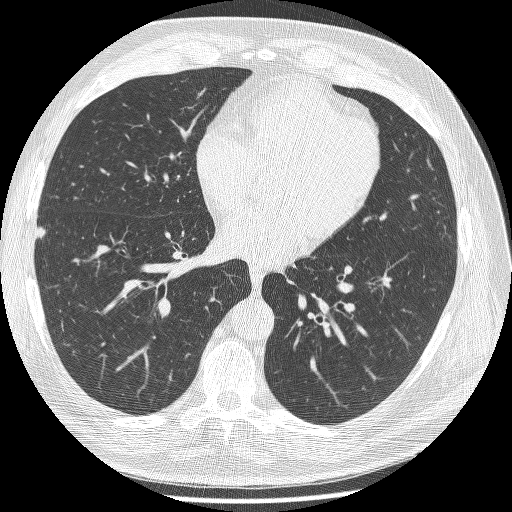
Low-dose screening chest CT, one axial slice; position 106 of 241 along the scan axis; reconstruction kernel BONE; 120 kVp; lung window (W 1500 / L -600 HU); 1.25 mm slice thickness; 512 × 512 image matrix, field of view 346 × 346 mm.
Structures marked on this image (manually delineated by an expert):
- lesion 1 (tumor, lower lobe of right lung): bounding box [x1, y1, x2, y2] px = [36, 227, 46, 240]